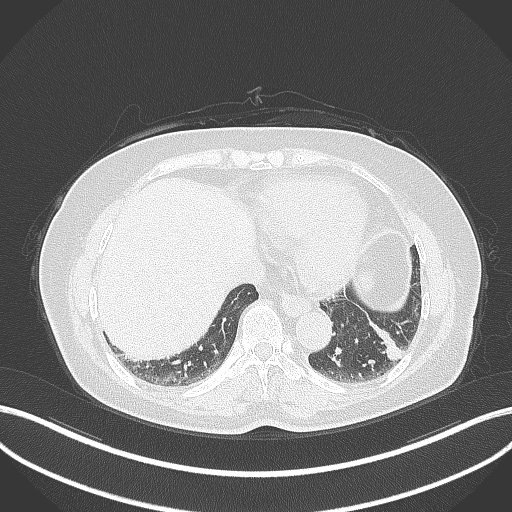
Chest CT, one axial slice. Reconstruction kernel B70f. Lung window (W 1500 / L -600 HU). 1 mm slice thickness. 512 × 512 image matrix, field of view 400 × 400 mm. Patient: female, 59 years. Case-level facts recorded for this patient, not image findings: clinical TNM (as recorded): T2a N0 M0; histopathological grade: G2-3.
Outlined on this slice (bounding box drawn by a radiologist):
- lung tumour (recorded histology: adenocarcinoma): bounding box [x1, y1, x2, y2] px = [362, 324, 406, 364]